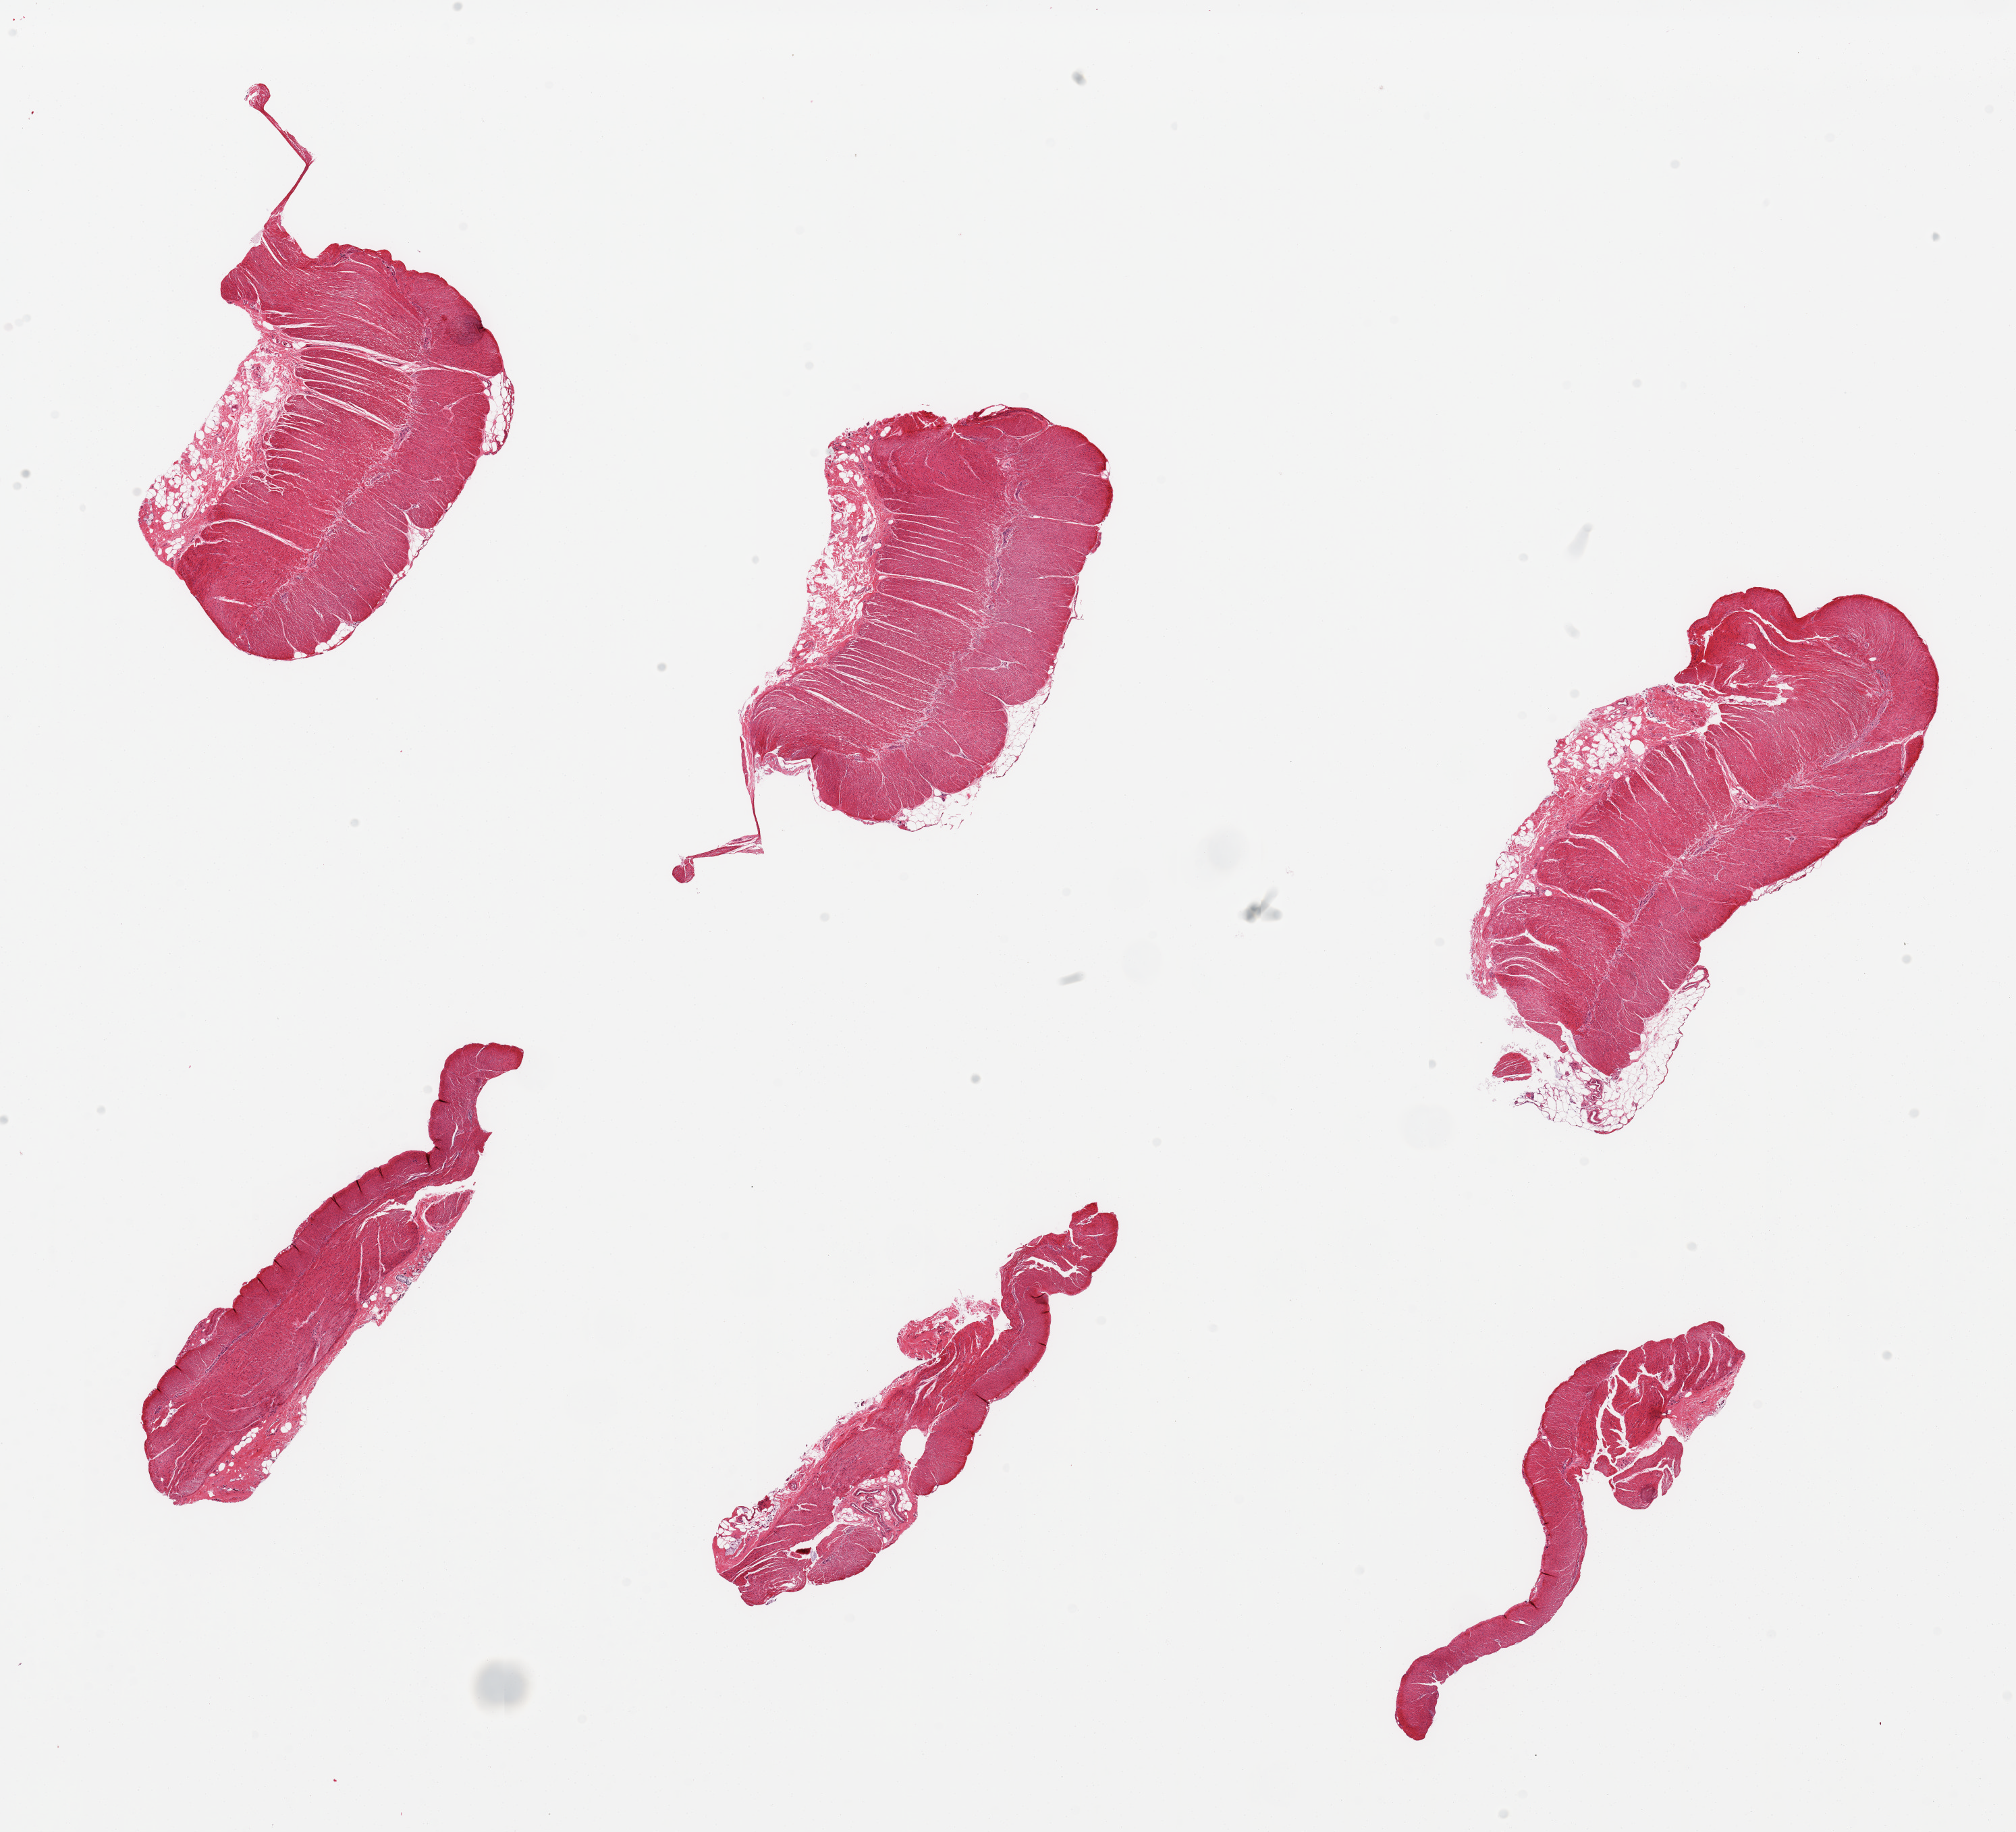
Digitized hematoxylin and eosin (H&E)-stained section, low-resolution overview of the scanned area, about 23.6 x 21.5 mm (from a 20x scan). PAXgene-fixed, paraffin-embedded tissue. Sampled site (target tissue): sigmoid colon. Donor tissue sample.
Review note (as recorded): 6 pieces; well trimmed muscle.